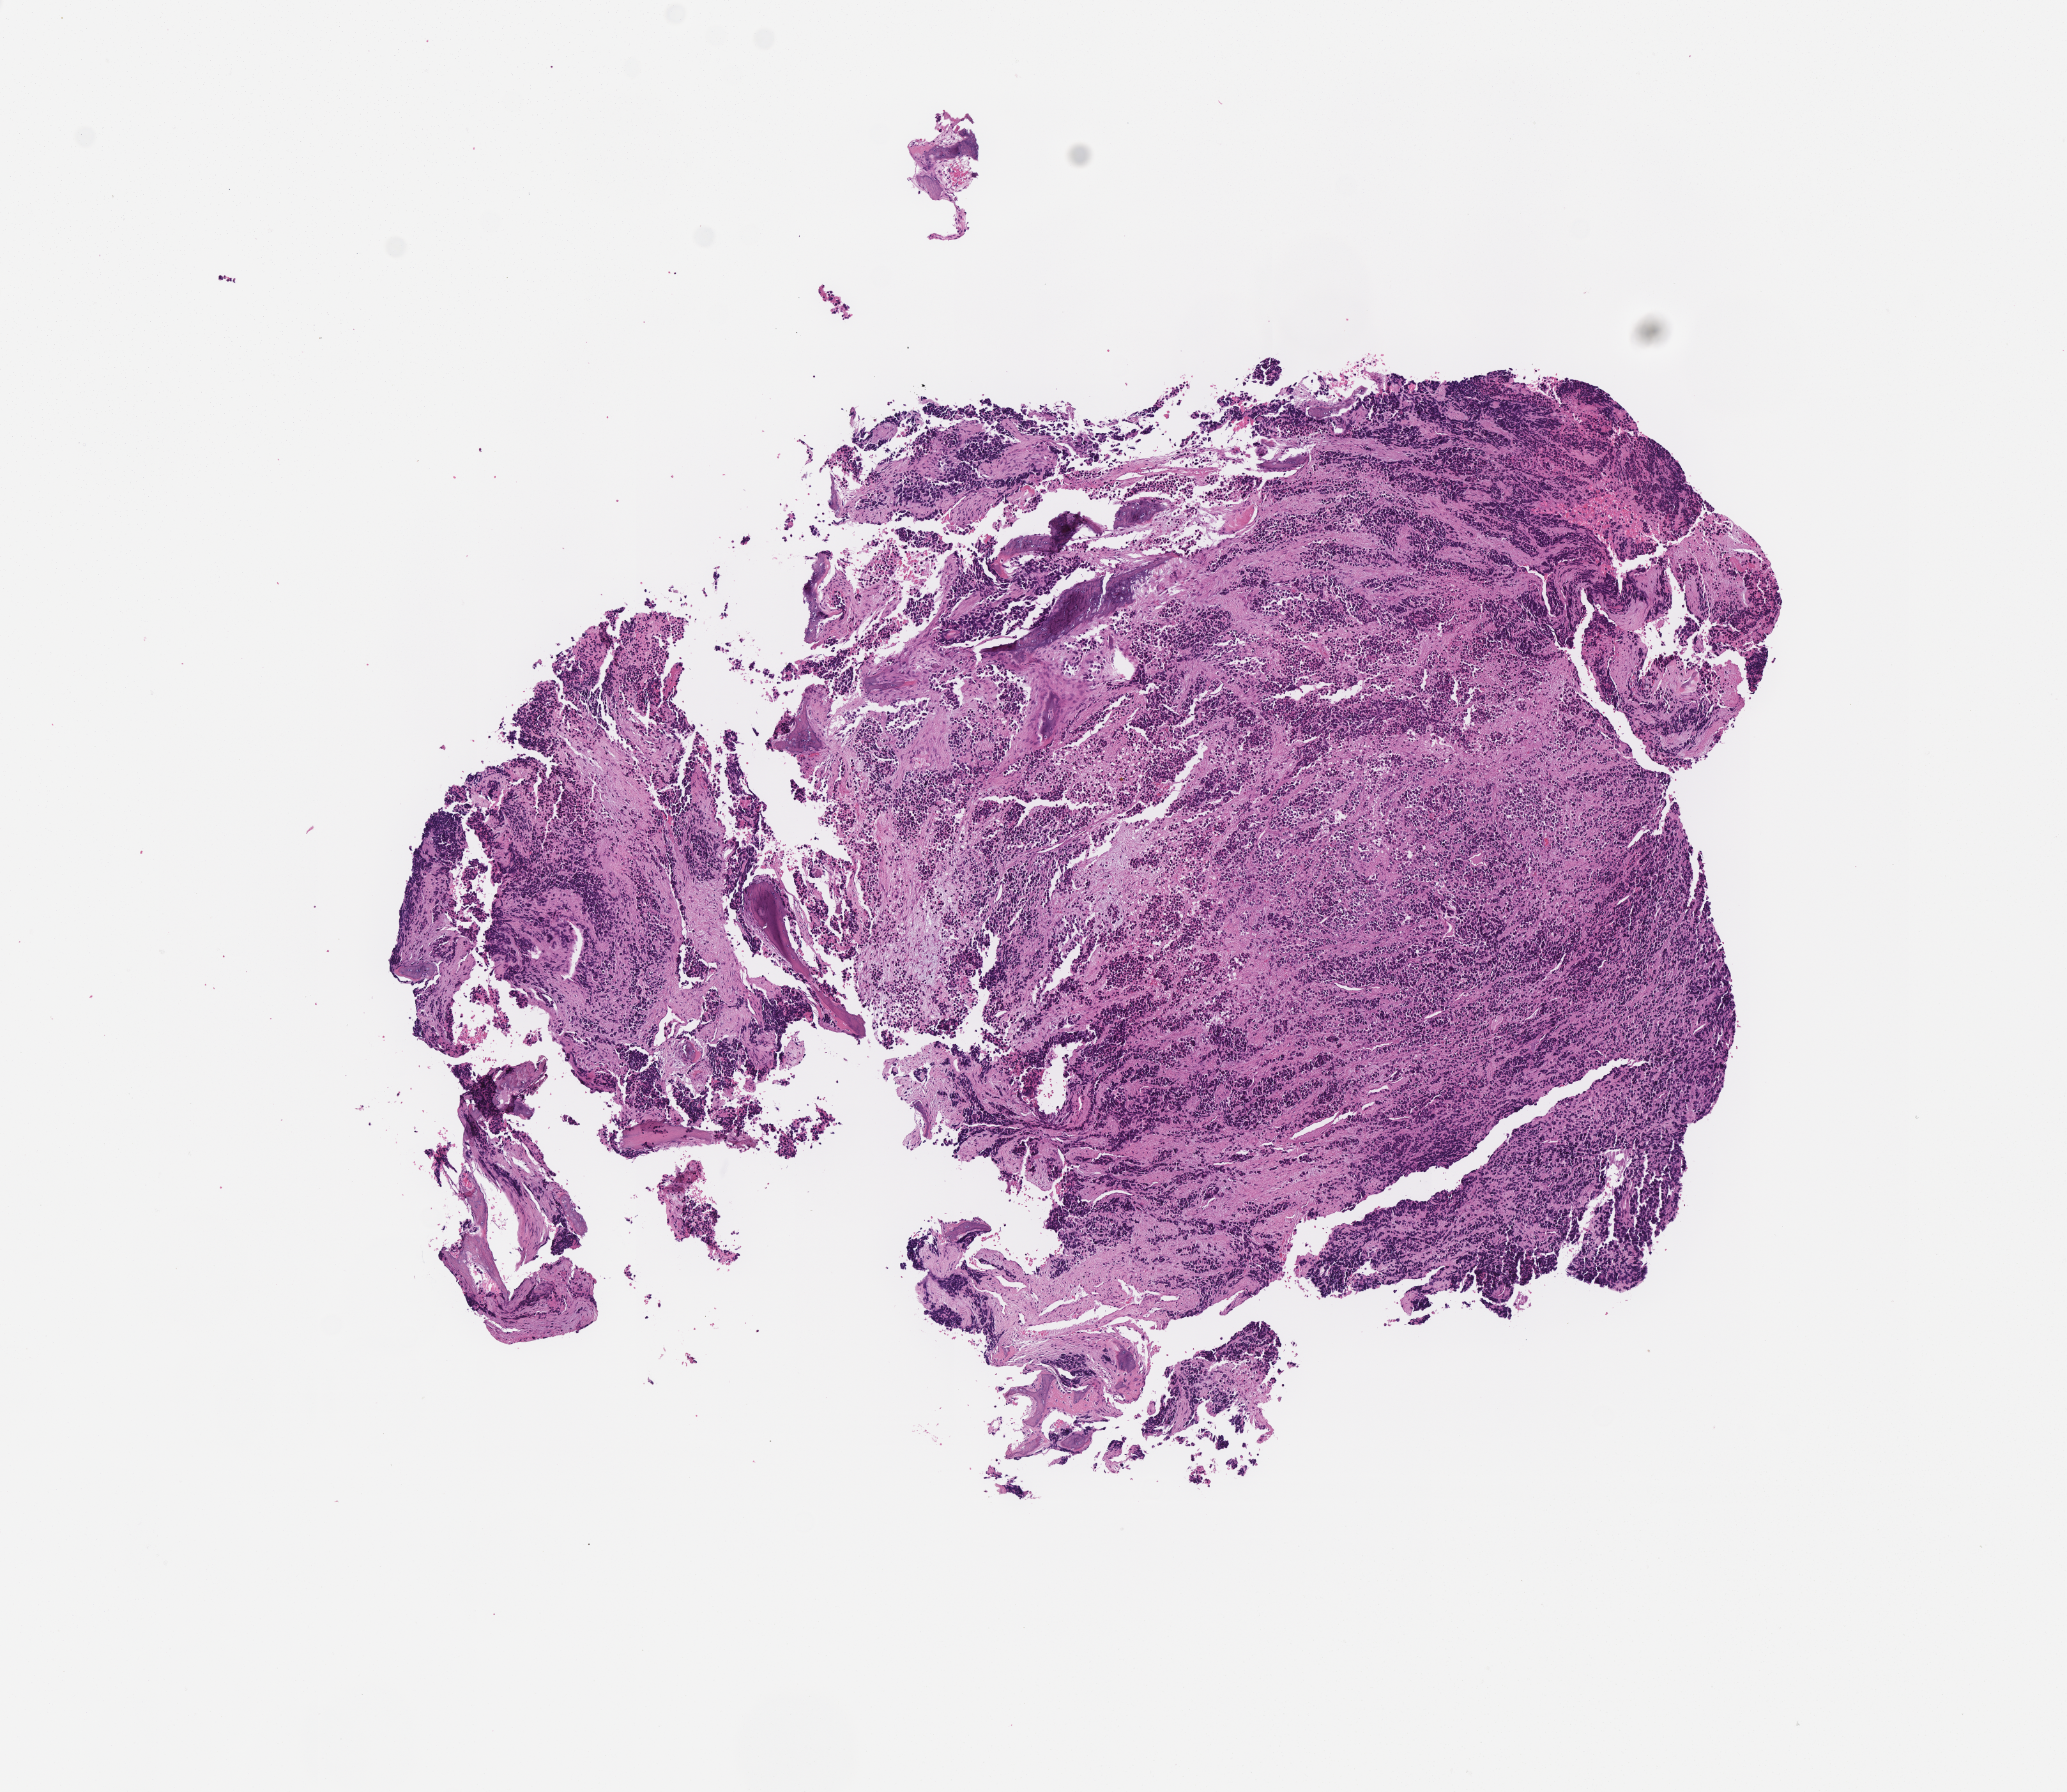
Digitized H&E-stained section of tumor tissue, a low-resolution overview of the entire scanned area, about 6.5 x 5.7 mm; FFPE section; site: nasal cavity, right. Patient: male, age 11.5 years at diagnosis.
Stage (as recorded): 3. Metastatic status at presentation (as recorded): non-metastatic. Diagnosis: rhabdomyosarcoma; histological classification: alveolar rhabdomyosarcoma.